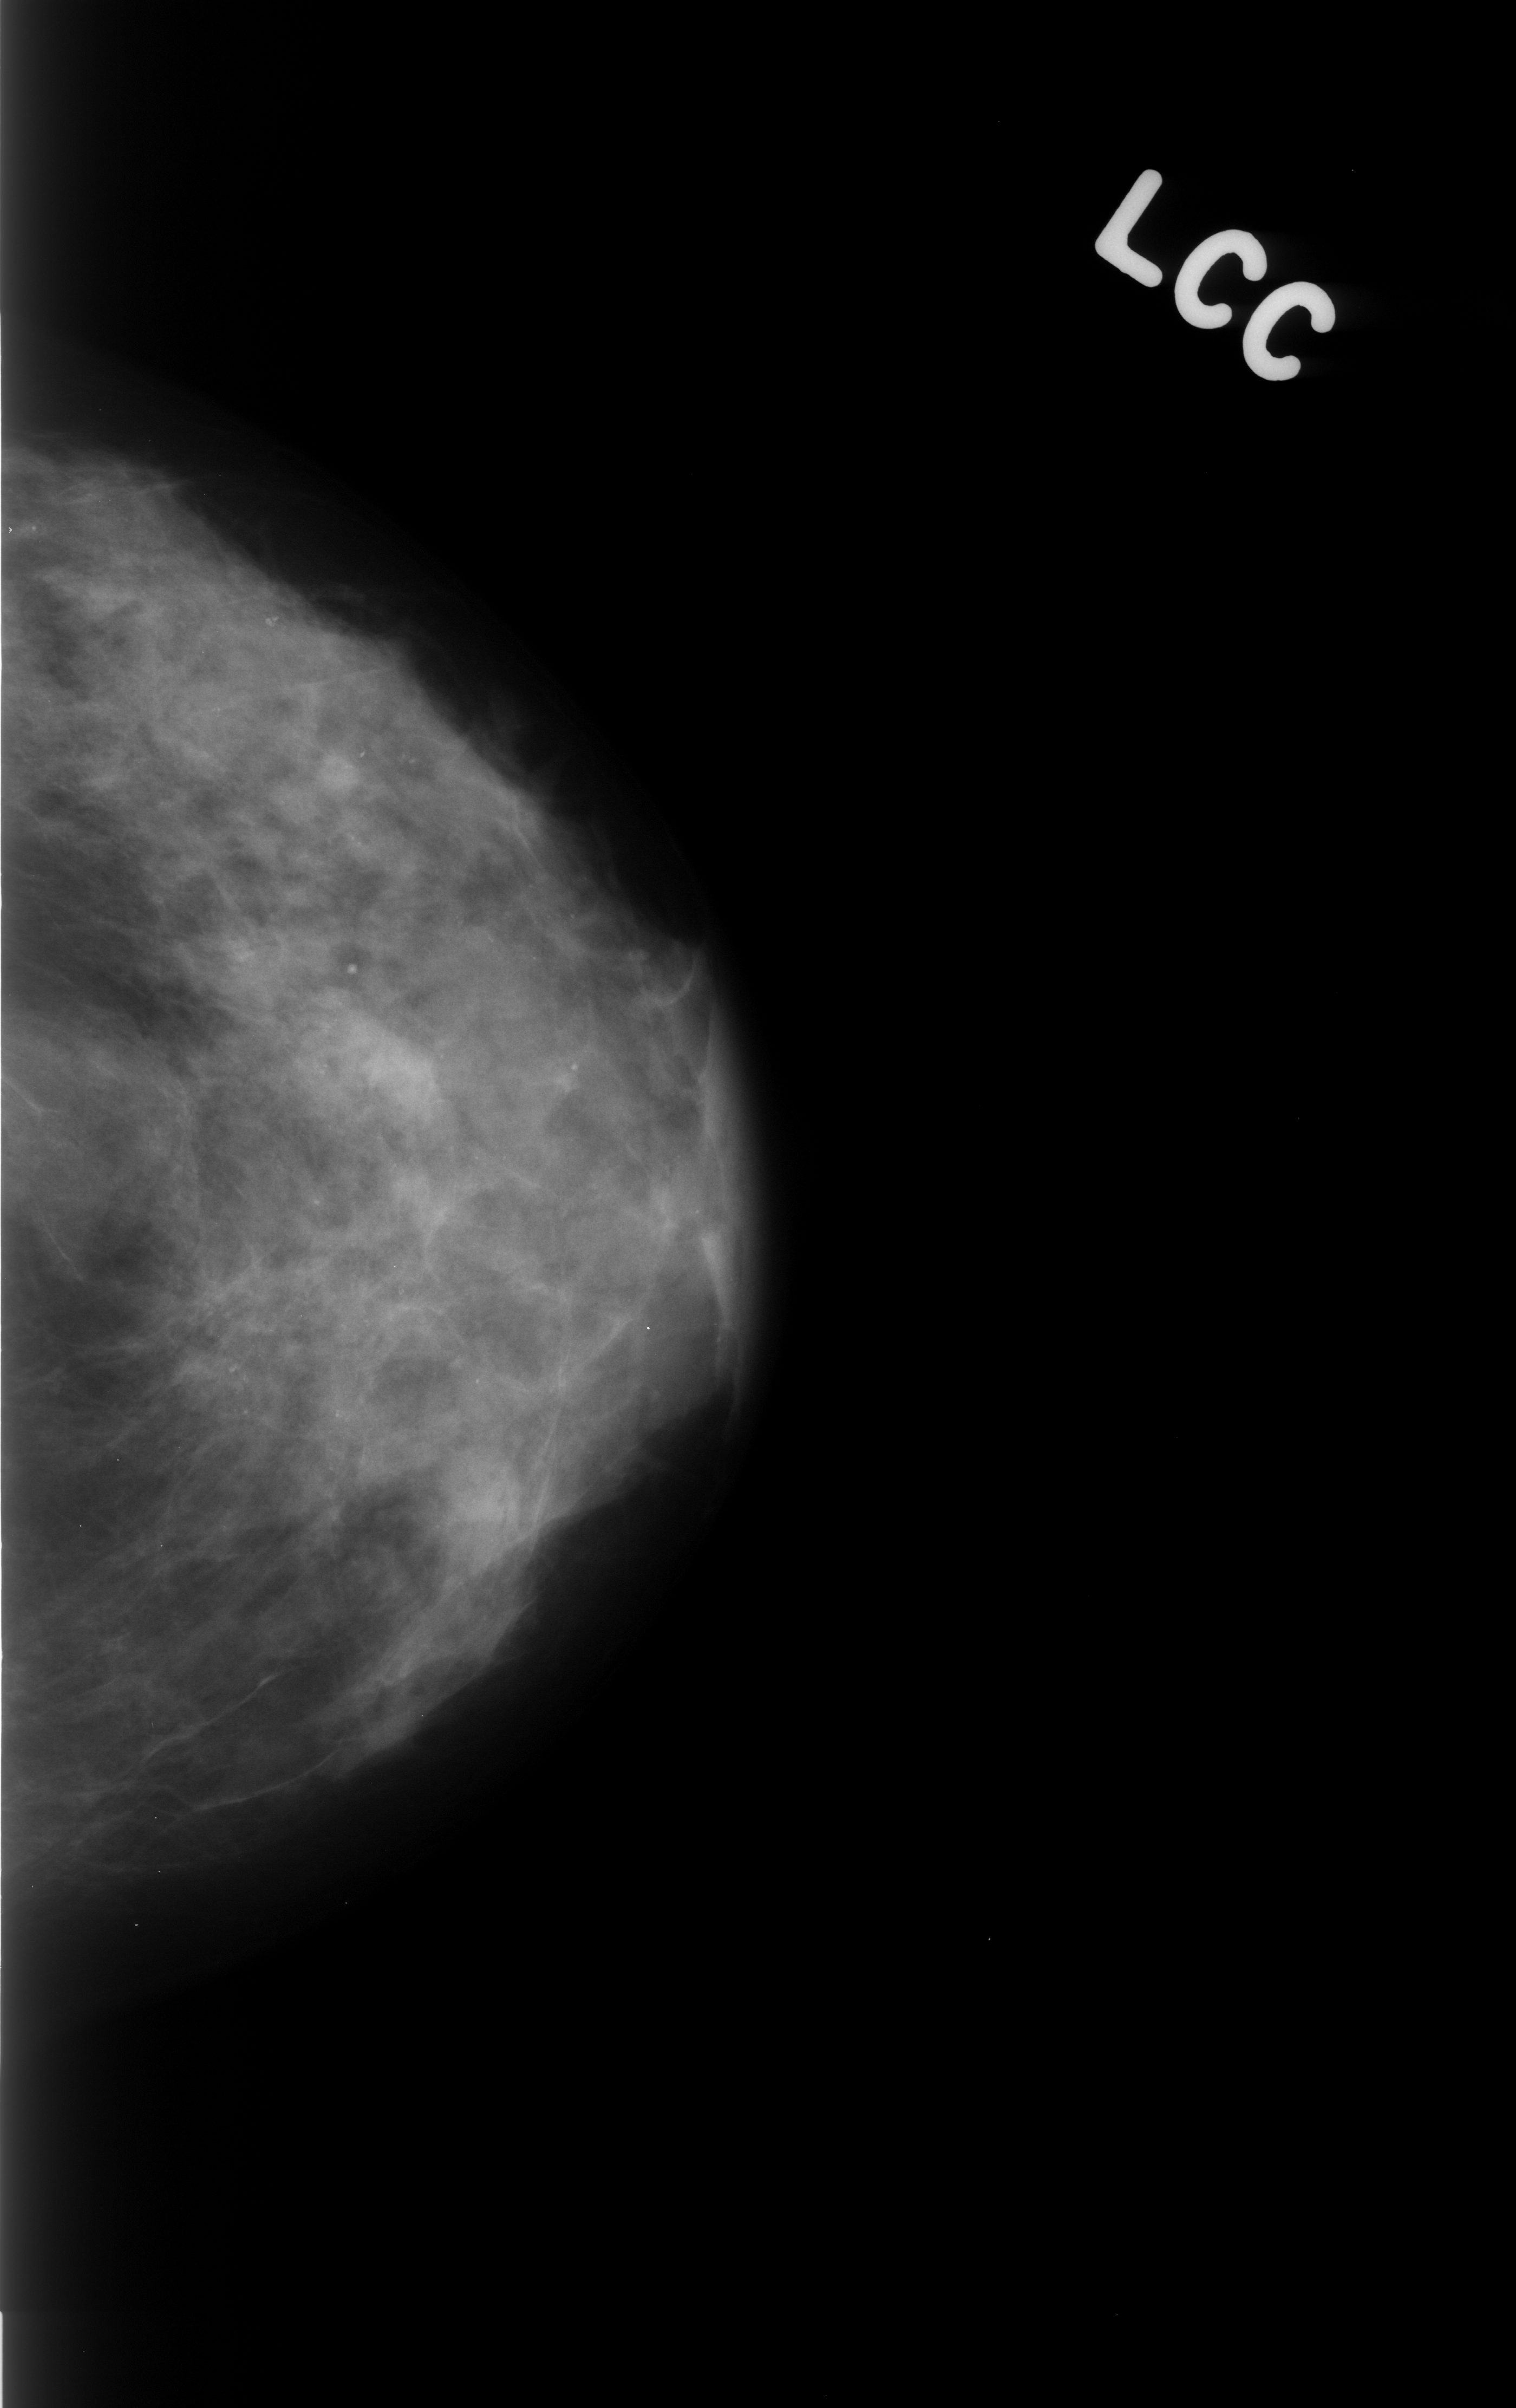
Scanned film-screen mammogram. Left breast. Craniocaudal (CC) view. Breast composition: heterogeneously dense (BI-RADS density category 3 of 4). 1516 × 2408 image matrix.
Marked abnormalities (boxes around the expert regions of interest):
- mass, shape round, margins ill defined; BI-RADS assessment category 4; subtlety rating 4 on a 1 (subtle) to 5 (obvious) scale; pathology result (as recorded, not read from the image): benign: bounding box [x1, y1, x2, y2] px = [0, 992, 173, 1270]